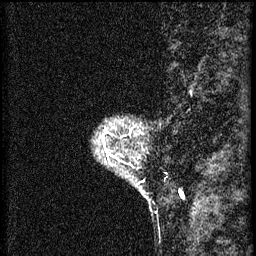
Breast MRI (dynamic contrast-enhanced), one sagittal slice; slice 6 of 60 in the series (ordered by position); 3 images stored at this slice position (order not interpretable as contrast timing); 1.5 T; TE 4.2 ms, TR 8.2 ms; 2 mm slice thickness; 256 × 256 image matrix, field of view 180 × 180 mm. Female patient, age 41 years.
Outlined on this slice (semi-automatic segmentation, software-assisted and operator-edited):
- analysis volume of interest (the breast-tissue region the enhancement analysis was run in; not a lesion): bounding box (x1, y1, x2, y2) in pixels: (98, 126, 148, 167)
- tumour enhancement mask (voxels above the 70 % enhancement threshold inside the analysis volume of interest): (103, 136, 108, 153)